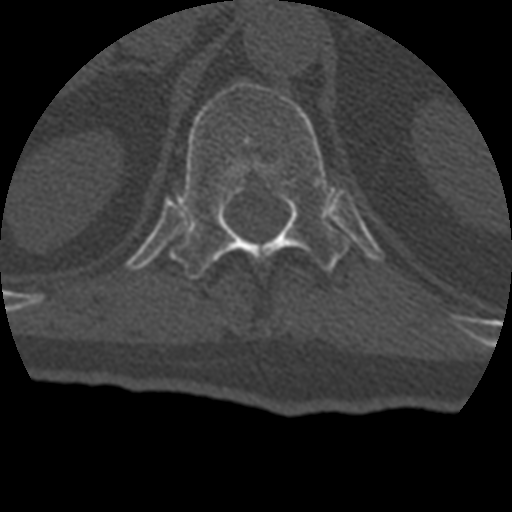
CT including the spine, one axial slice; reconstruction kernel STANDARD; bone window (W 1800 / L 400 HU); 1.25 mm slice thickness; 512 × 512 image matrix, field of view 160 × 160 mm. Patient age 69 years. From the clinical record (not read from this slice): primary cancer: prostate.
Annotated regions visible in this slice (semi-automatically segmented with operator editing):
- T12 vertebra: bounding box (x1, y1, x2, y2) in pixels: (171, 82, 349, 279)